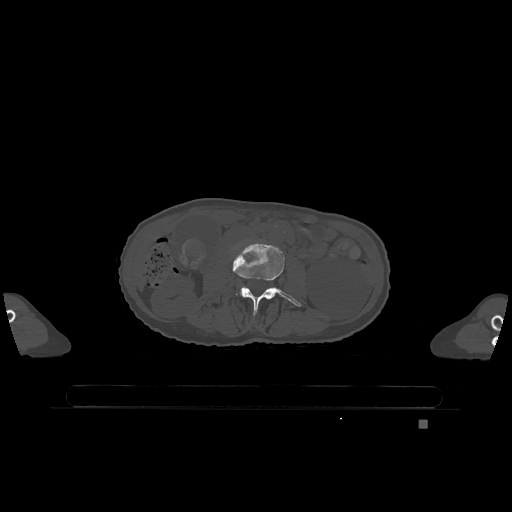
CT including the spine, one axial slice. Position 351 of 1317 along the scan axis. Bone window (W 1800 / L 400 HU). 0.5 mm slice thickness. 512 × 512 image matrix, field of view 500 × 500 mm. Patient: female, 74 years. From the clinical record (not read from this slice): primary cancer: lung.
Structures marked on this image (semi-automatically segmented with operator editing):
- L3 vertebra: bounding box (x1, y1, x2, y2) in pixels: (232, 243, 301, 315)